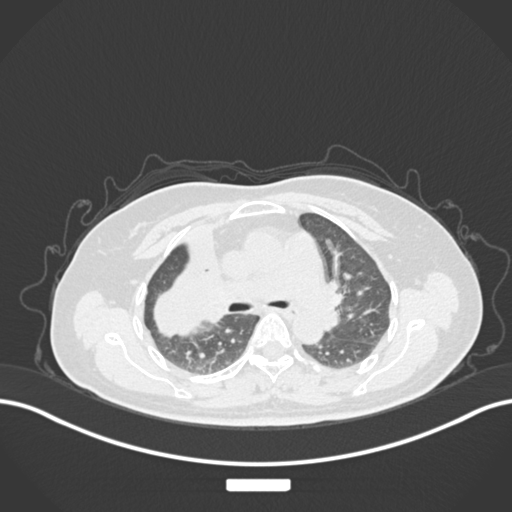
Chest CT, one axial slice. Slice 97 of 177 in the series (ordered by position). 120 kVp. Lung window (W 1500 / L -600 HU). 1 mm slice thickness. 512 × 512 image matrix, field of view 400 × 400 mm. Patient: female, 60 years. From the clinical record (not read from this slice): clinical TNM (as recorded): T3 N1 M1.
Structures marked on this image (bounding box drawn by a radiologist):
- lung tumour (recorded histology: adenocarcinoma): bounding box [x1, y1, x2, y2] px = [140, 250, 253, 350]